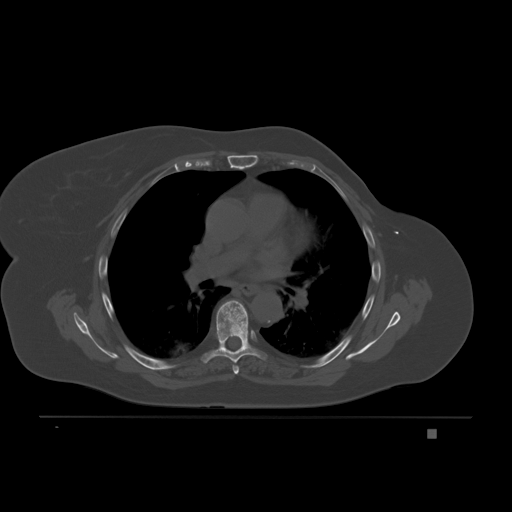
CT including the spine, one axial slice; position 137 of 221 along the scan axis; bone window (W 1800 / L 400 HU); 512 × 512 image matrix. Patient: female, 63 years. From the clinical record (not read from this slice): primary cancer: breast.
Outlined on this slice (semi-automatically segmented with operator editing):
- T5 vertebra: box from (x=233, y=362) to (x=239, y=374) px
- T6 vertebra: (x=201, y=300)–(x=267, y=363)